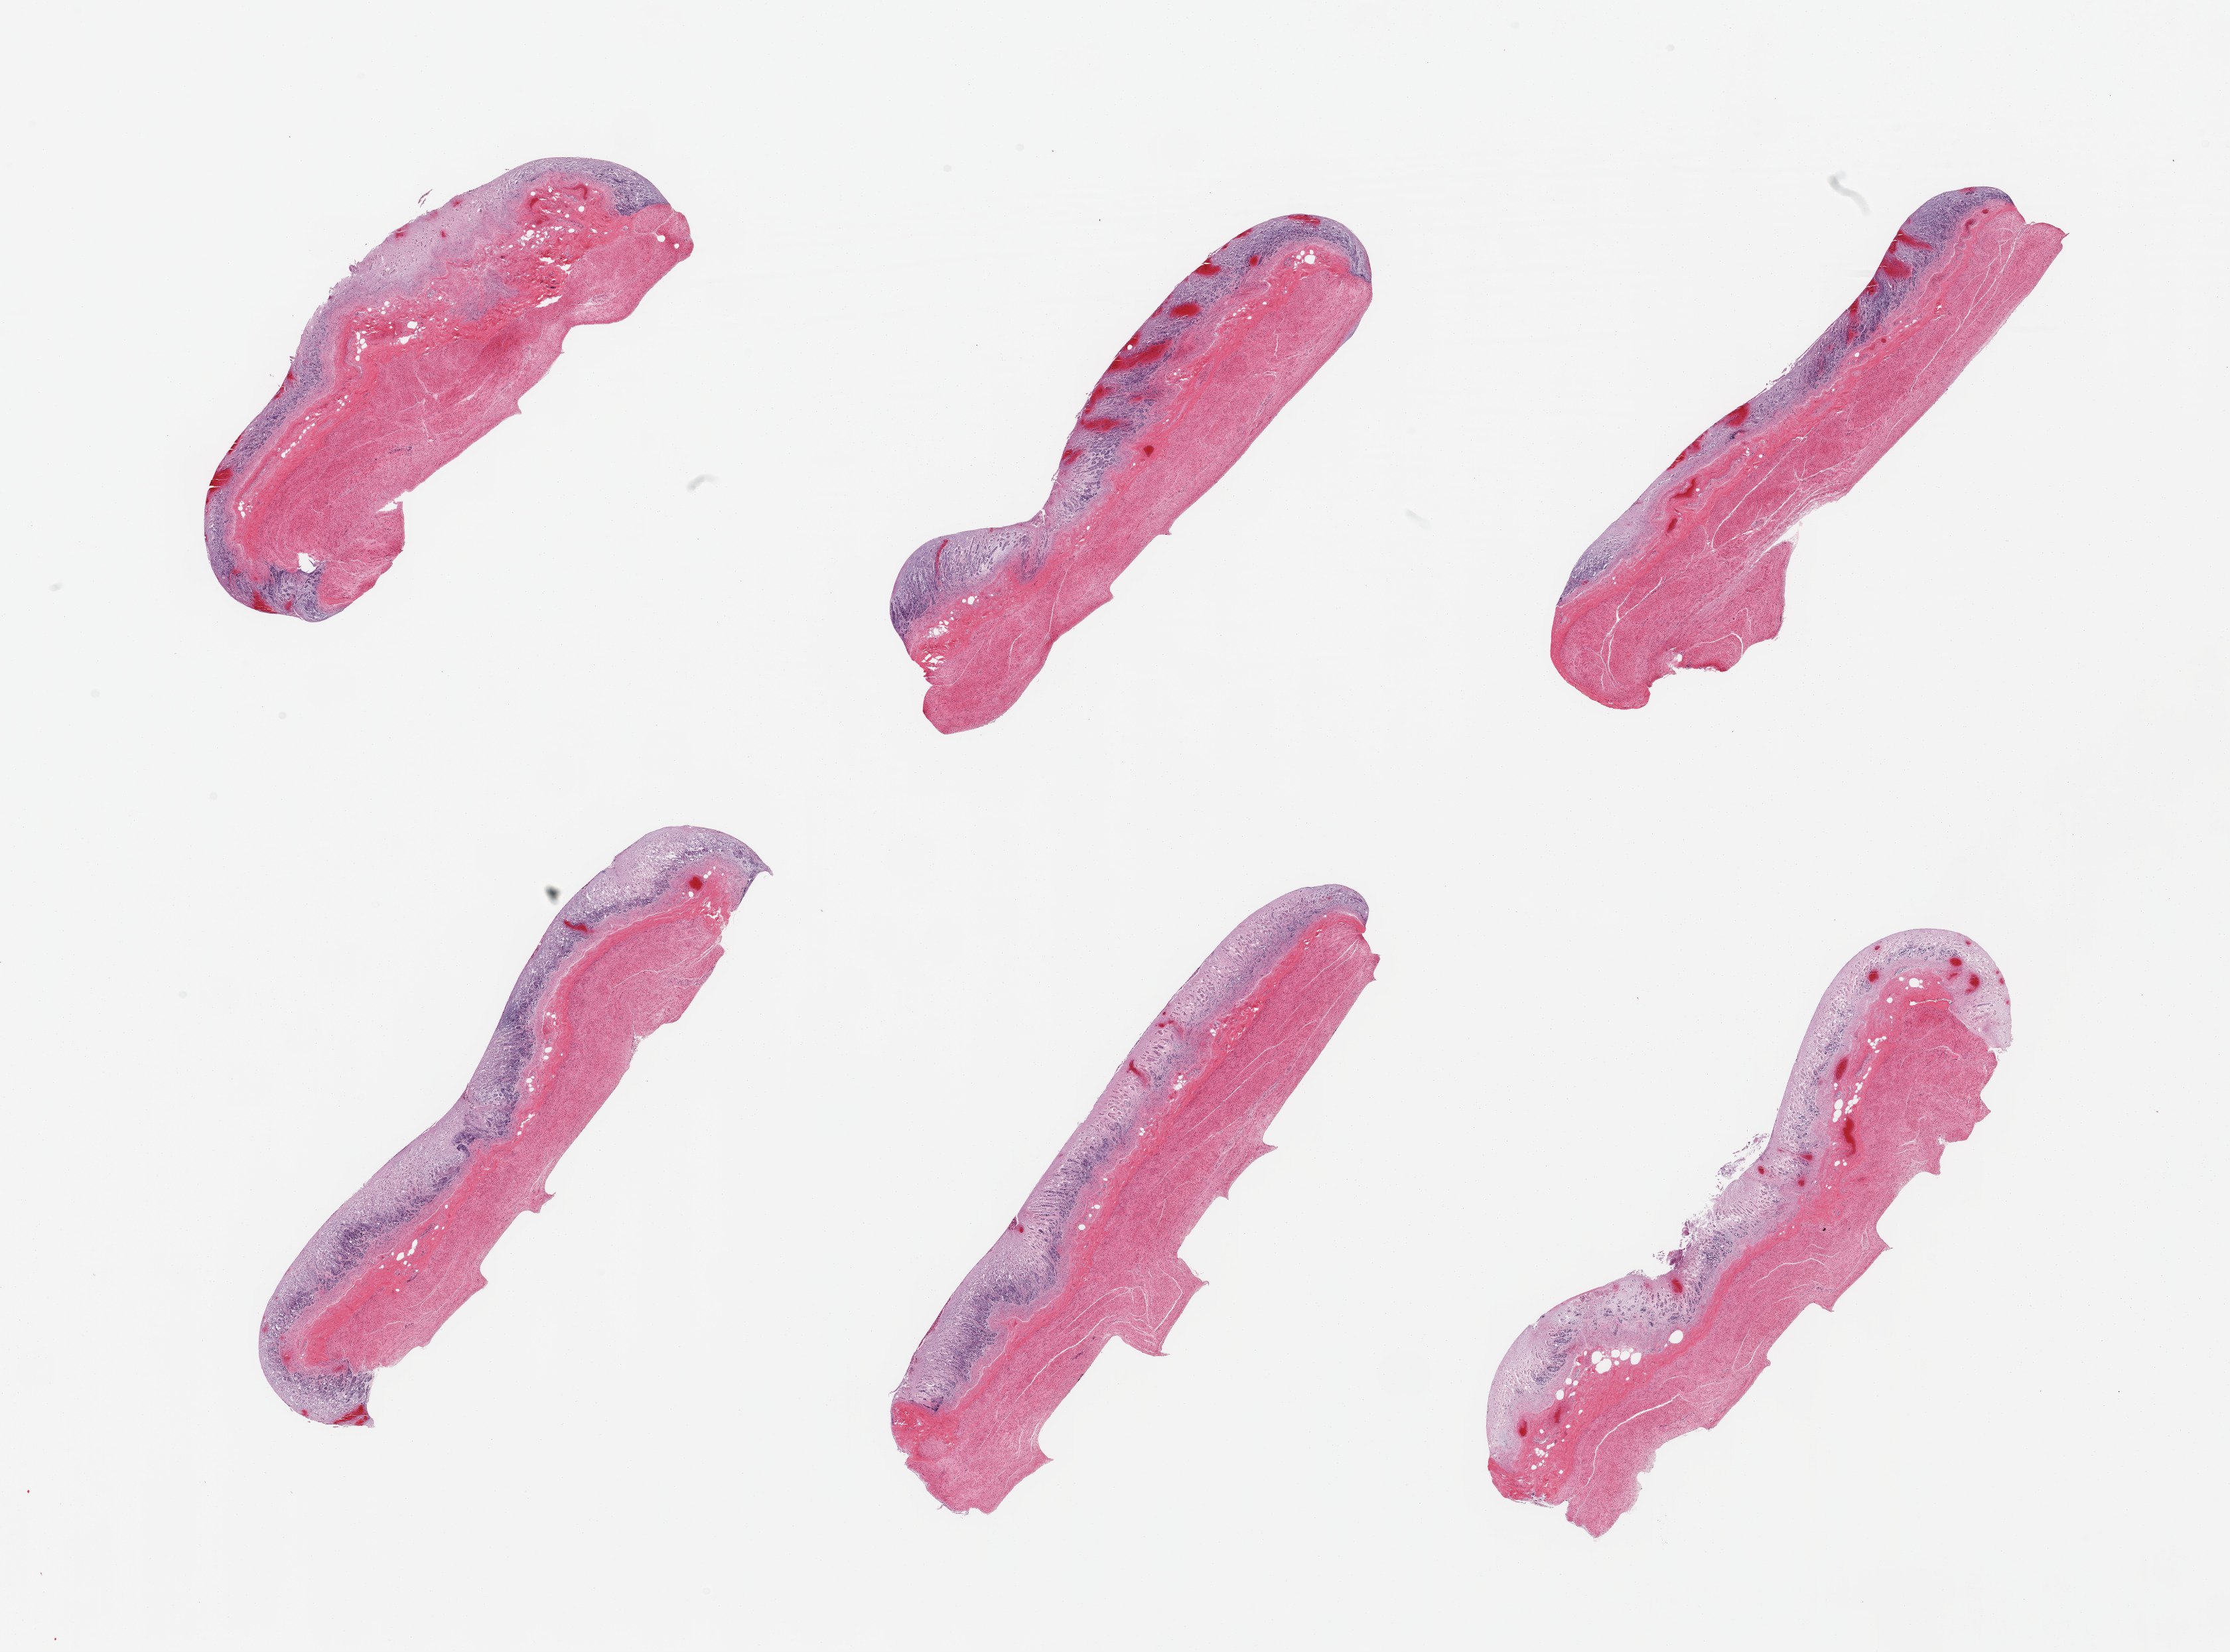
Digitized hematoxylin and eosin (H&E)-stained section — low-resolution overview of the scanned area, about 26.6 x 19.7 mm, PAXgene-fixed paraffin-embedded (PFPE) section, section of stomach (target tissue), tissue donor sample. Male donor.
Review note (as recorded): 6 pieces; full thickness, mucosa is autolyzed with focal hemorrhage, muscularis is better preserved.